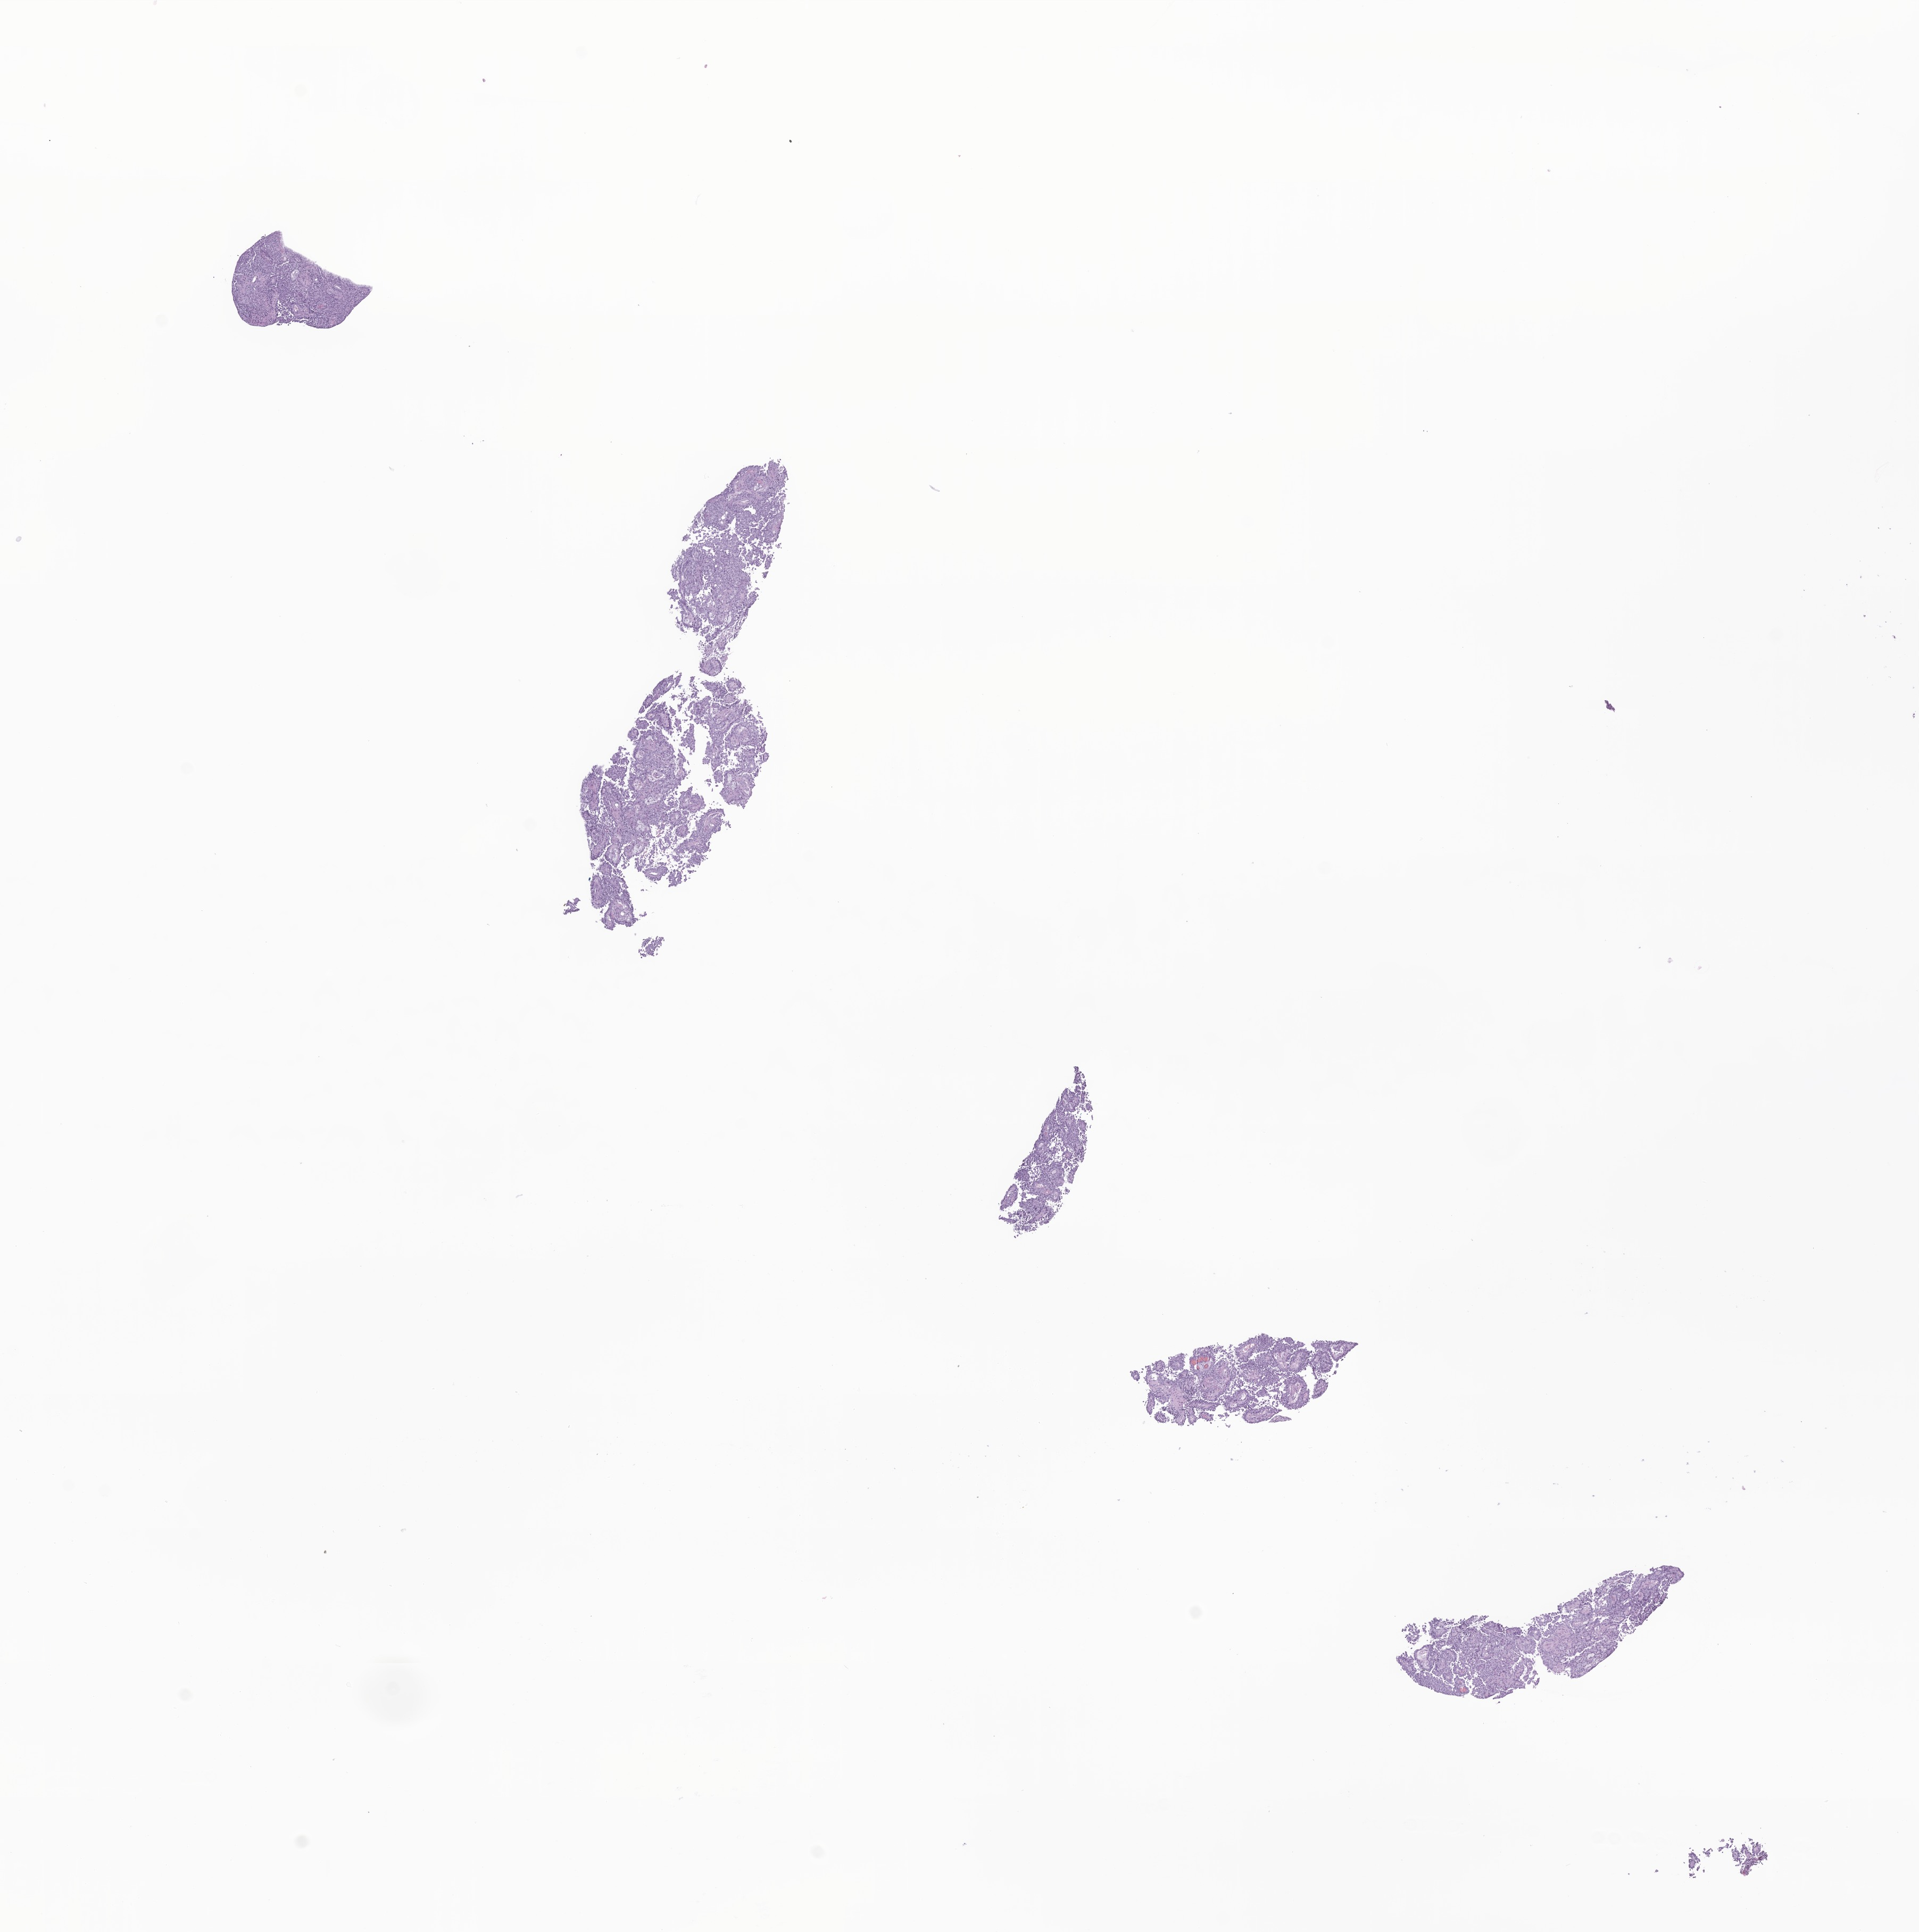
Haematoxylin and eosin whole-slide image of tumor tissue from the brain — whole scanned area (about 15.2 x 15.3 mm) shown as a low-resolution overview. Formalin-fixed, paraffin-embedded (FFPE) tissue. Patient male; age 205 months (17 years 1 month).
Recorded diagnosis: Neoplasm, uncertain whether benign or malignant.